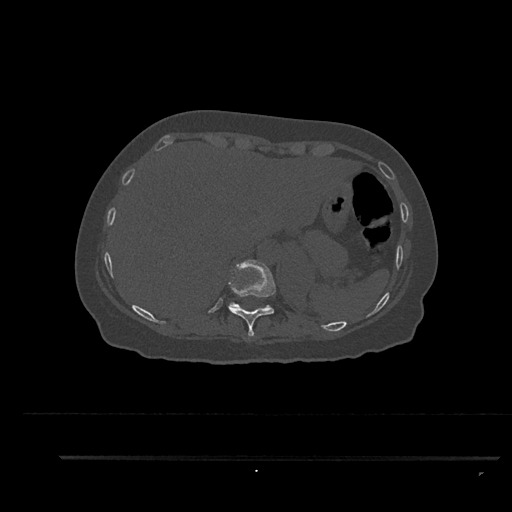
CT including the spine, one axial slice; position 352 of 797 along the scan axis; 120 kVp; bone window (W 1800 / L 400 HU); 0.5 mm slice thickness; 512 × 512 image matrix, field of view 408 × 408 mm. Female patient, age 44 years. From the clinical record (not read from this slice): primary cancer: renal.
Outlined on this slice (semi-automatic segmentation, software-assisted and operator-edited):
- T10 vertebra: bounding box <228,259,276,337> (left, top, right, bottom; pixels)
- T11 vertebra: <229,302,269,306>